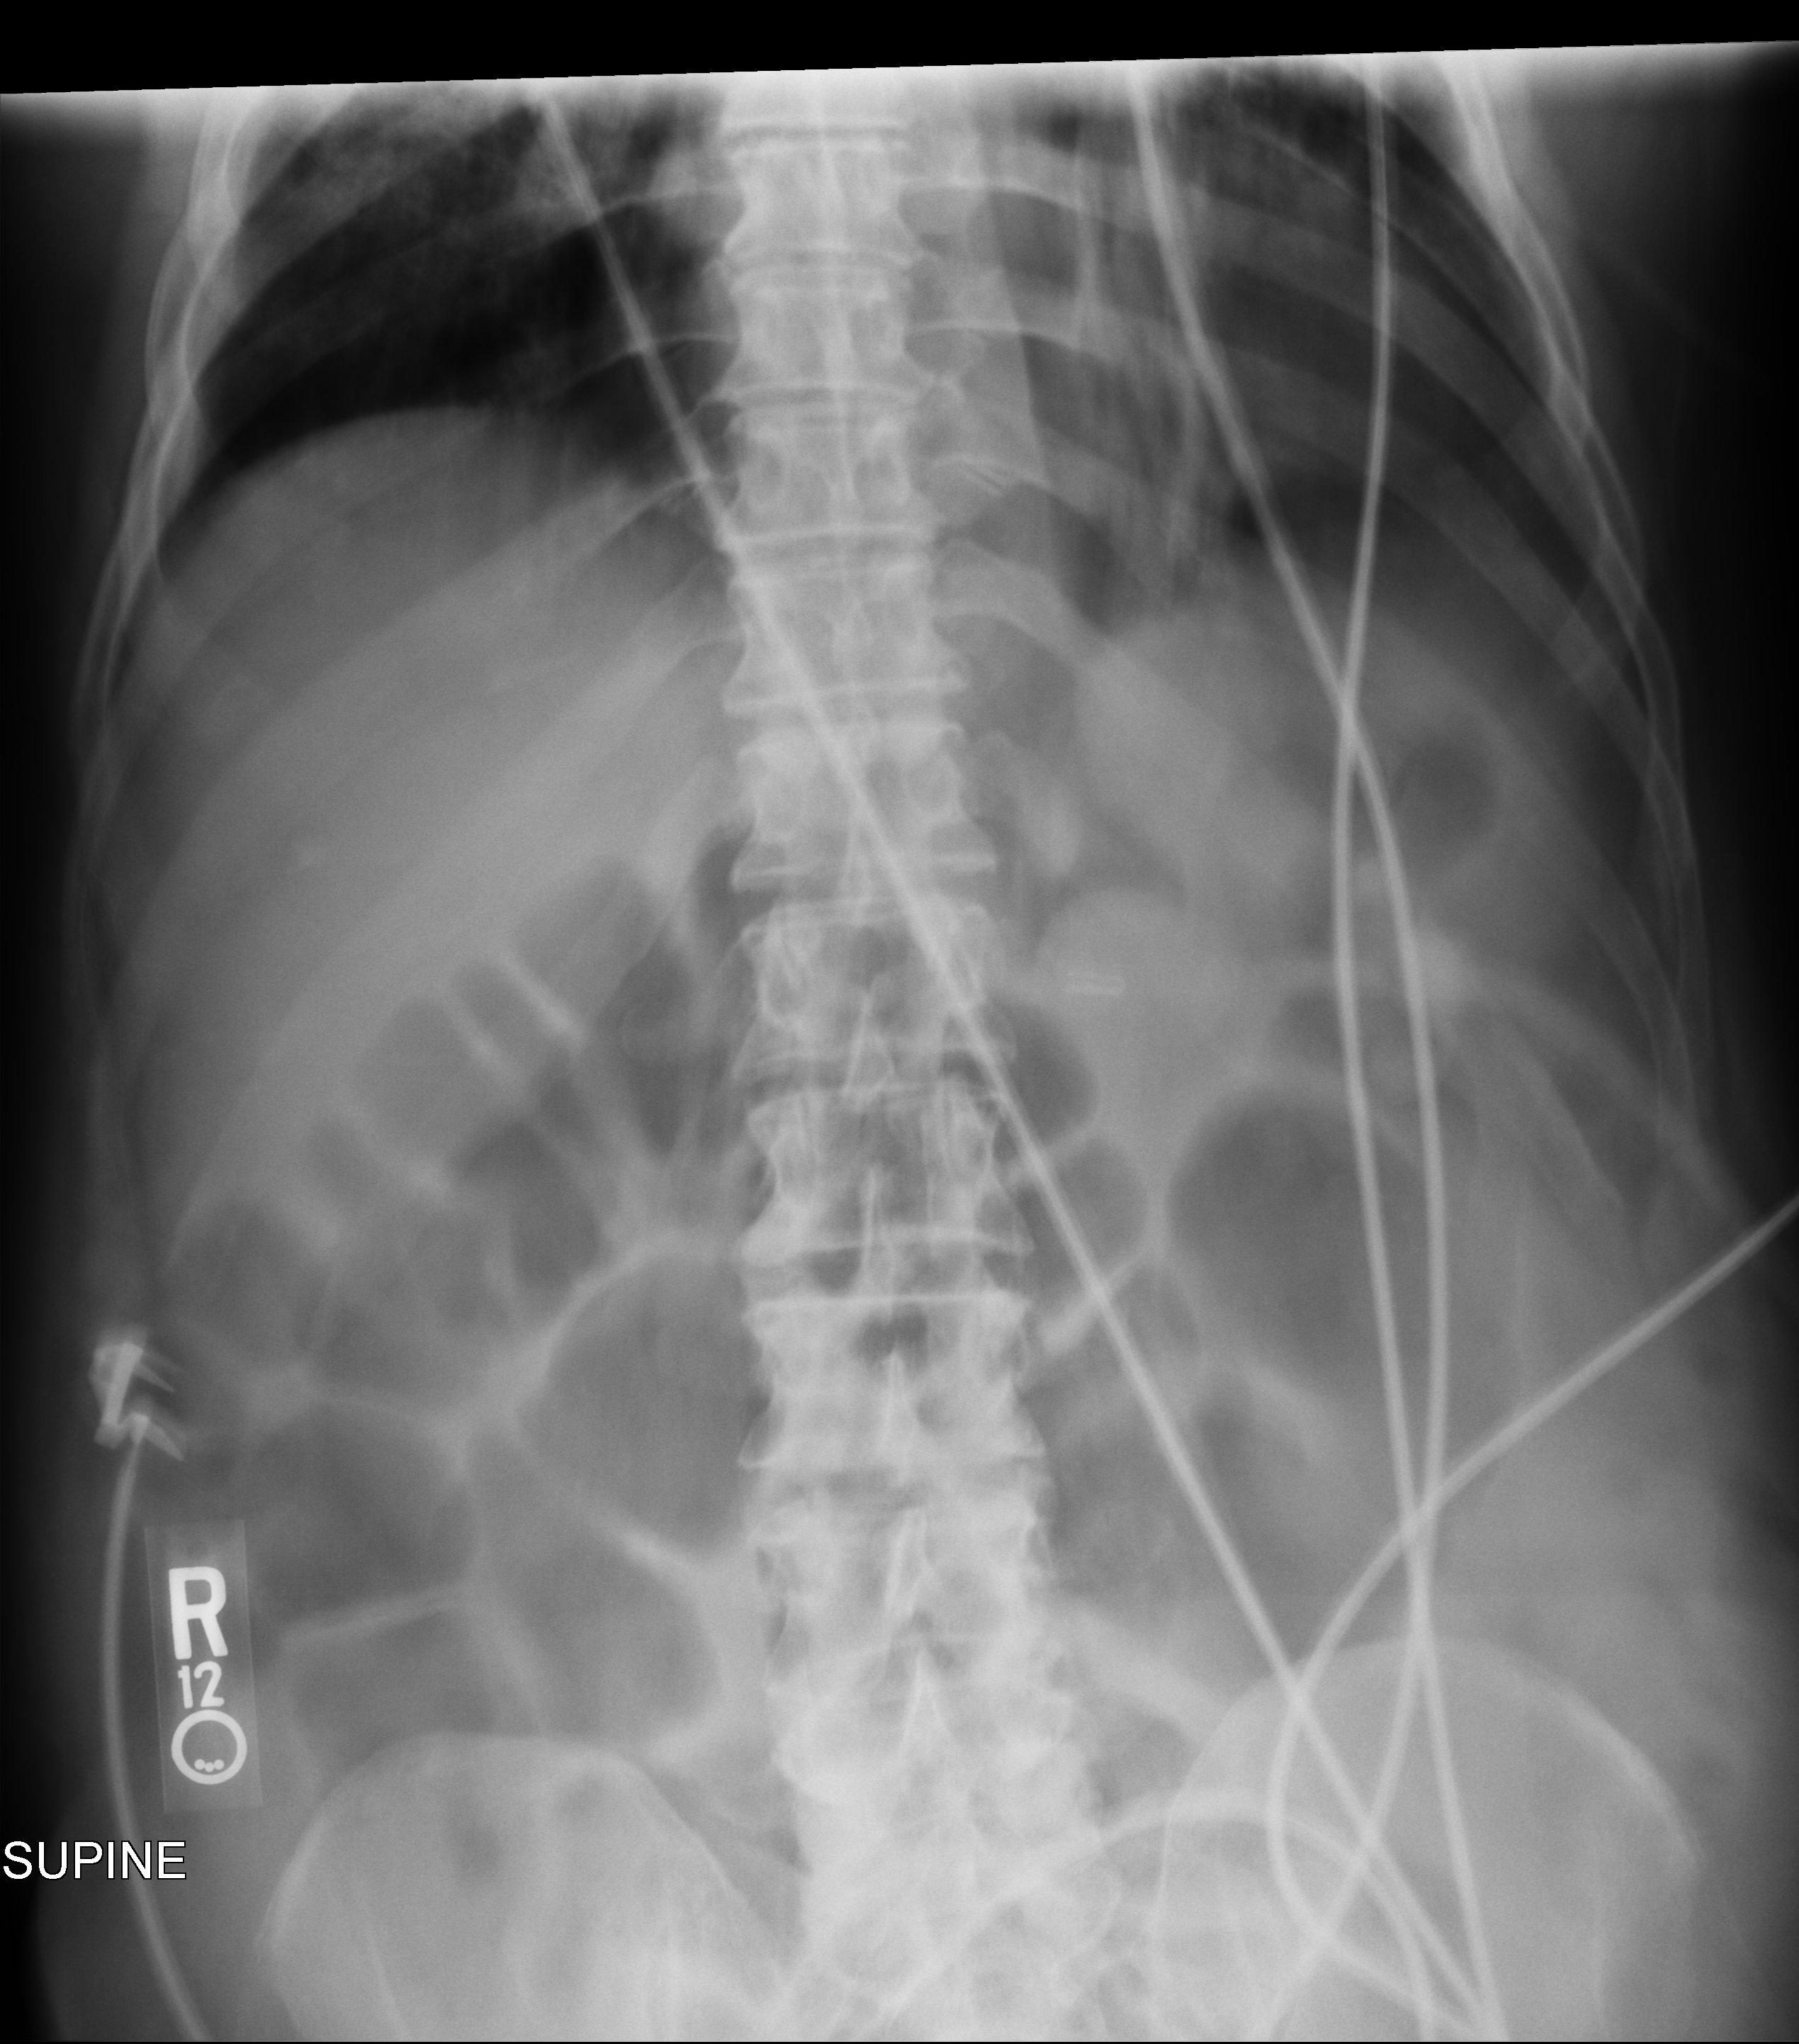
Abdomen X-ray (portable); anteroposterior (AP) projection. Patient hospitalised with COVID-19; male, aged 60–74 years.
From the hospital-stay record, not from the radiograph (when in the stay this image was taken is not recorded): other chronic lung disease (admission record): no.